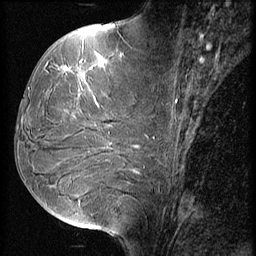
Breast MRI (dynamic contrast-enhanced), one sagittal slice; position 26 of 56 along the scan axis; 3 images stored at this slice position (order not interpretable as contrast timing); 1.5 T; TE 4.2 ms, TR 9 ms; 2.5 mm slice thickness; 256 × 256 image matrix, field of view 180 × 180 mm. Female patient, age 51 years. Case-level facts recorded for this patient, not image findings: setting: breast cancer imaged before/during neoadjuvant chemotherapy; receptor status: HR-positive, HER2-negative.
Outlined on this slice (semi-automatic segmentation, software-assisted and operator-edited):
- analysis volume of interest (the breast-tissue region the enhancement analysis was run in; not a lesion): box from (x=23, y=56) to (x=156, y=165) px
- tumour enhancement mask (voxels above the 140 % enhancement threshold inside the analysis volume of interest): (x=63, y=56)–(x=120, y=107)